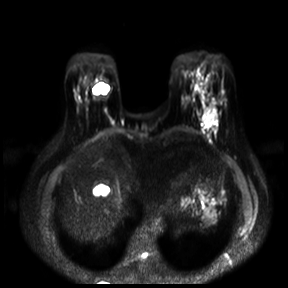
Breast MRI, one axial slice; position 6 of 30 along the scan axis; diffusion-weighted series; image 2 of 4 stored at this slice position (different b-values; order by instance number); 3 T; 288 × 288 image matrix, field of view 360 × 360 mm. Female patient.
Outlined on this slice (expert manual segmentation):
- tumour on diffusion-weighted imaging: box from (x=203, y=108) to (x=216, y=126) px